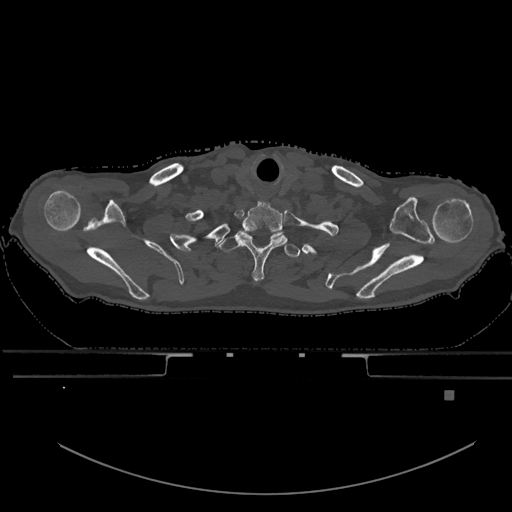
CT including the spine, one axial slice; slice 560 of 969 in the series (ordered by position); bone window (W 1800 / L 400 HU); 0.5 mm slice thickness; 512 × 512 image matrix, field of view 456 × 456 mm. Patient: male, 82 years. From the clinical record (not read from this slice): primary cancer: prostate; vertebrae with lytic lesions (as recorded): T11, T9, T8, T2.
Structures marked on this image (semi-automatically segmented with operator editing):
- T1 vertebra: bounding box (x1, y1, x2, y2) in pixels: (219, 234, 300, 259)